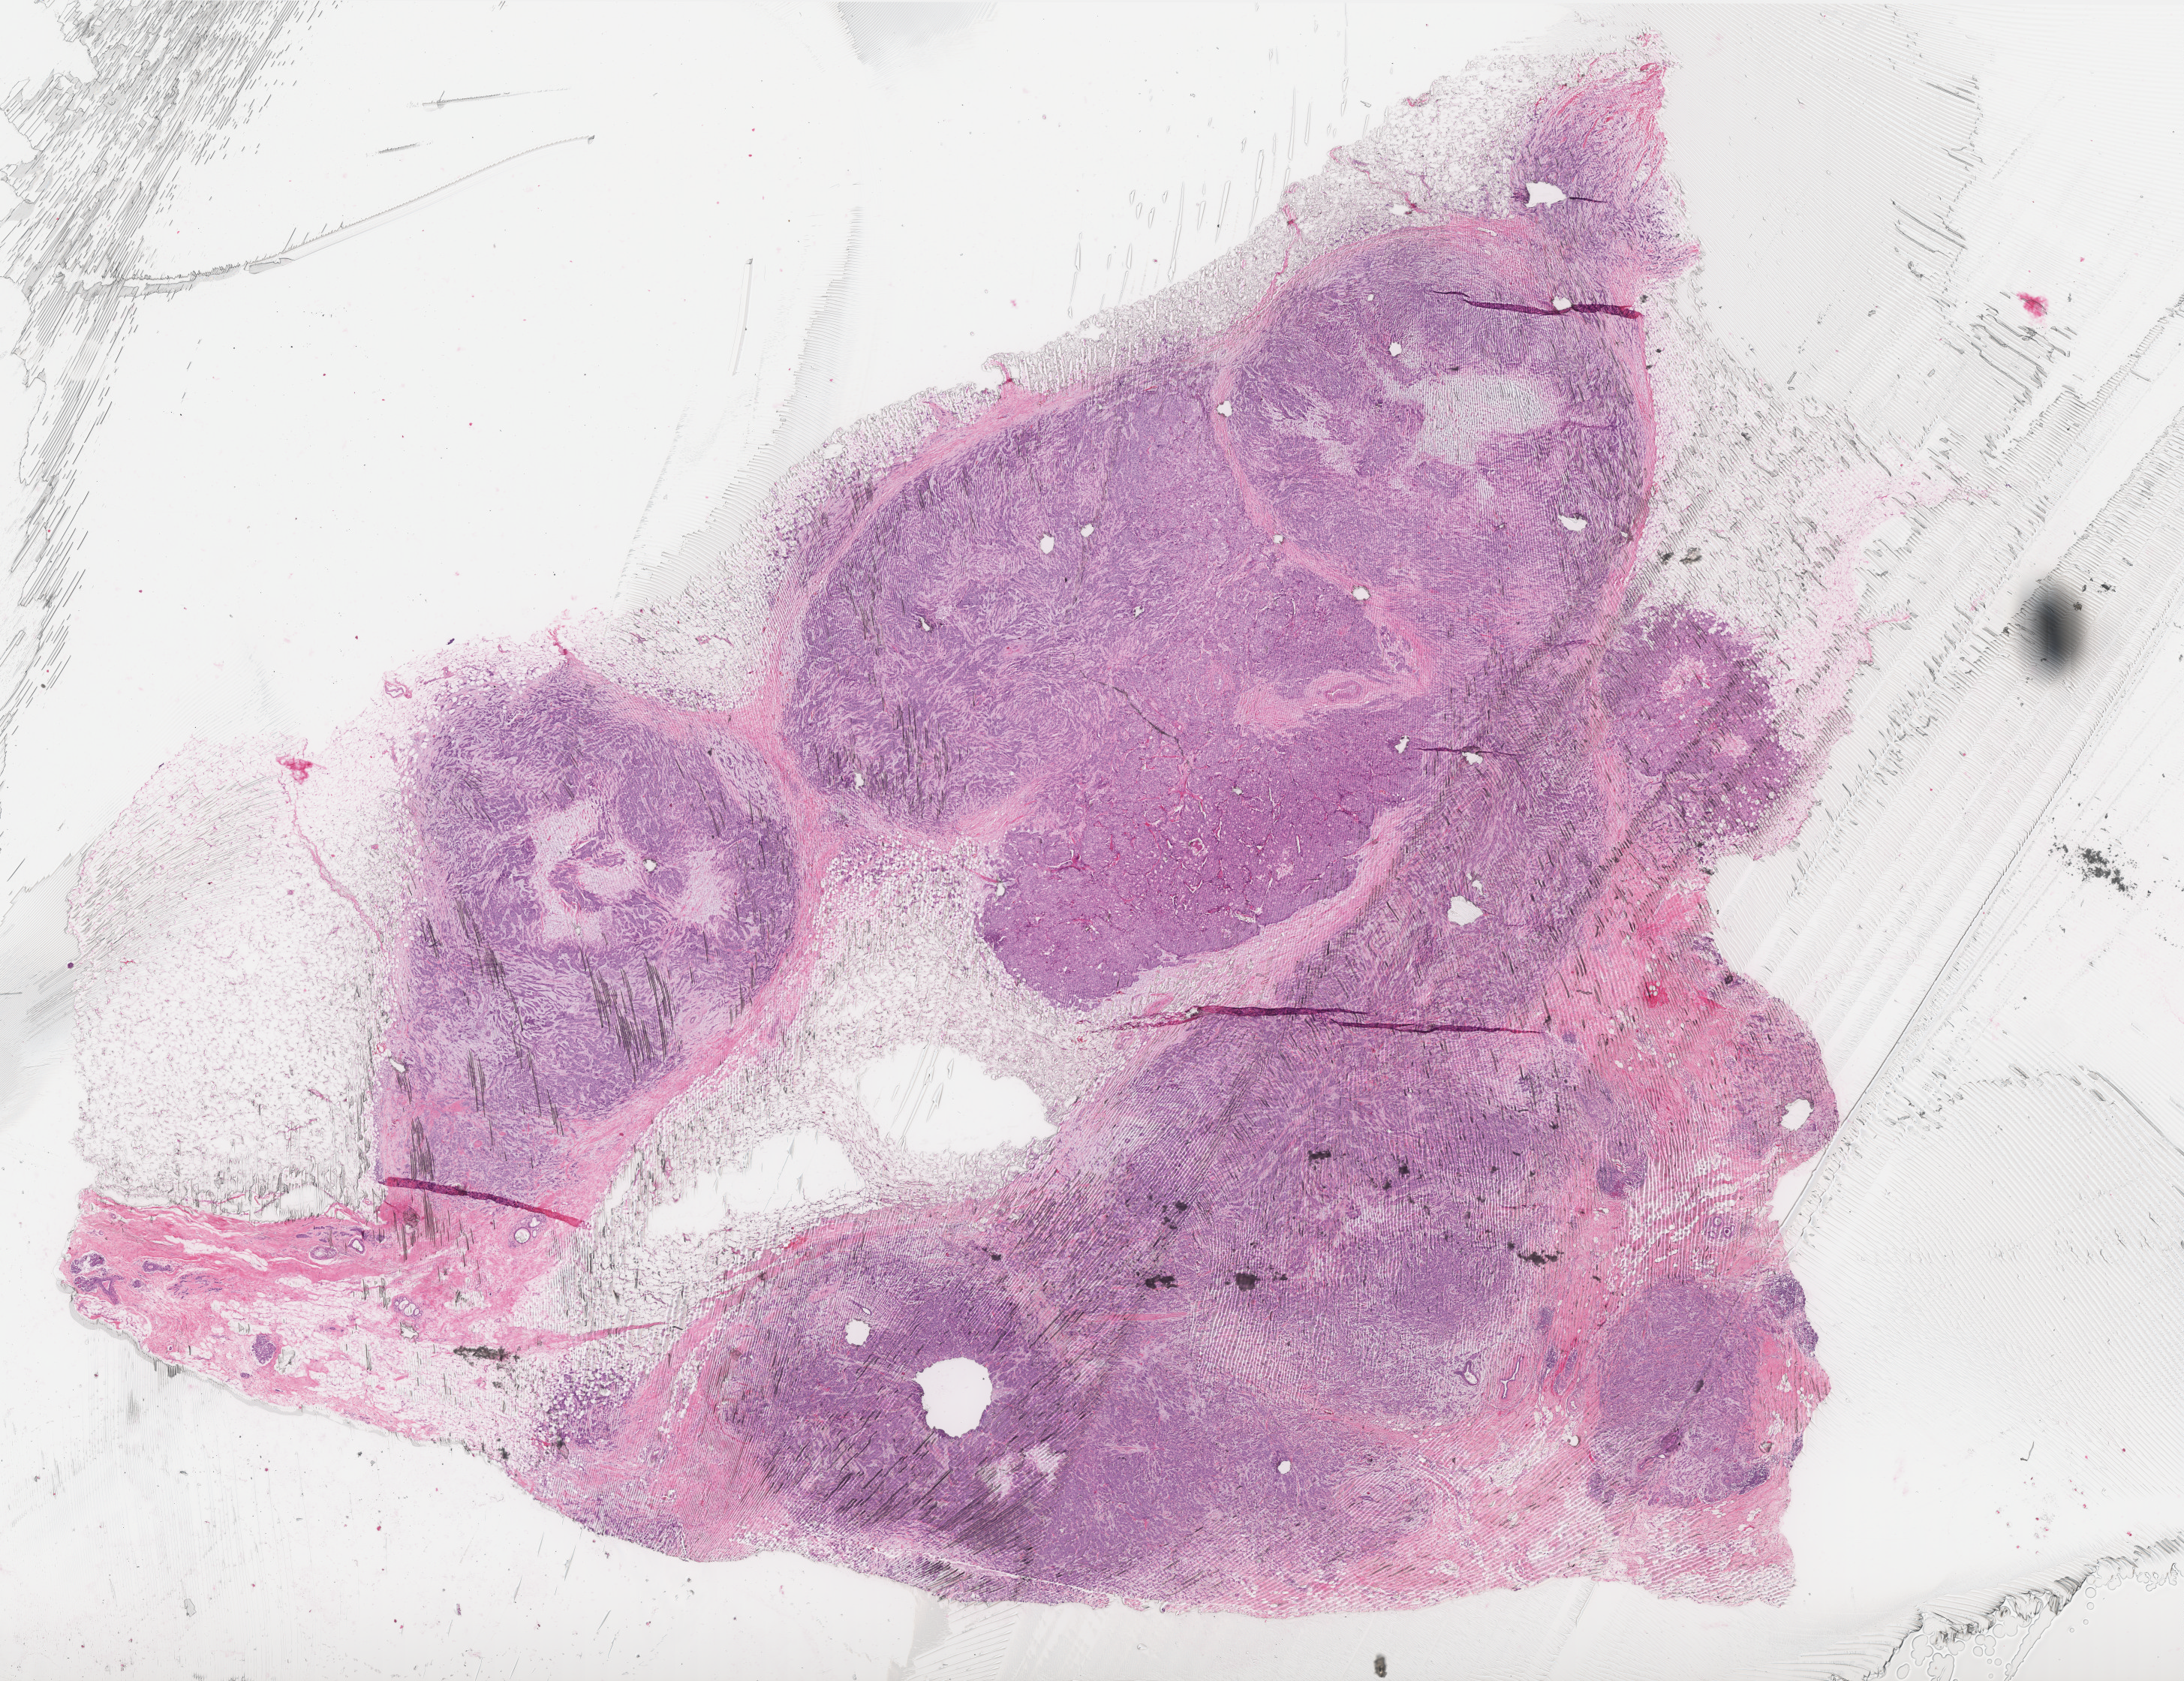
Hematoxylin and eosin (H&E) stained whole-slide image, low-resolution overview of the scanned area, about 23.3 x 18.0 mm, FFPE section, sample: primary tumour, breast. Female patient; age at initial diagnosis 64 years.
• TNM: T3 N3 M1
• AJCC pathologic stage: IV (3rd edition)
• histologic diagnosis: Infiltrating duct carcinoma, NOS
• lymph nodes positive (case pathology): 8 of 15 examined